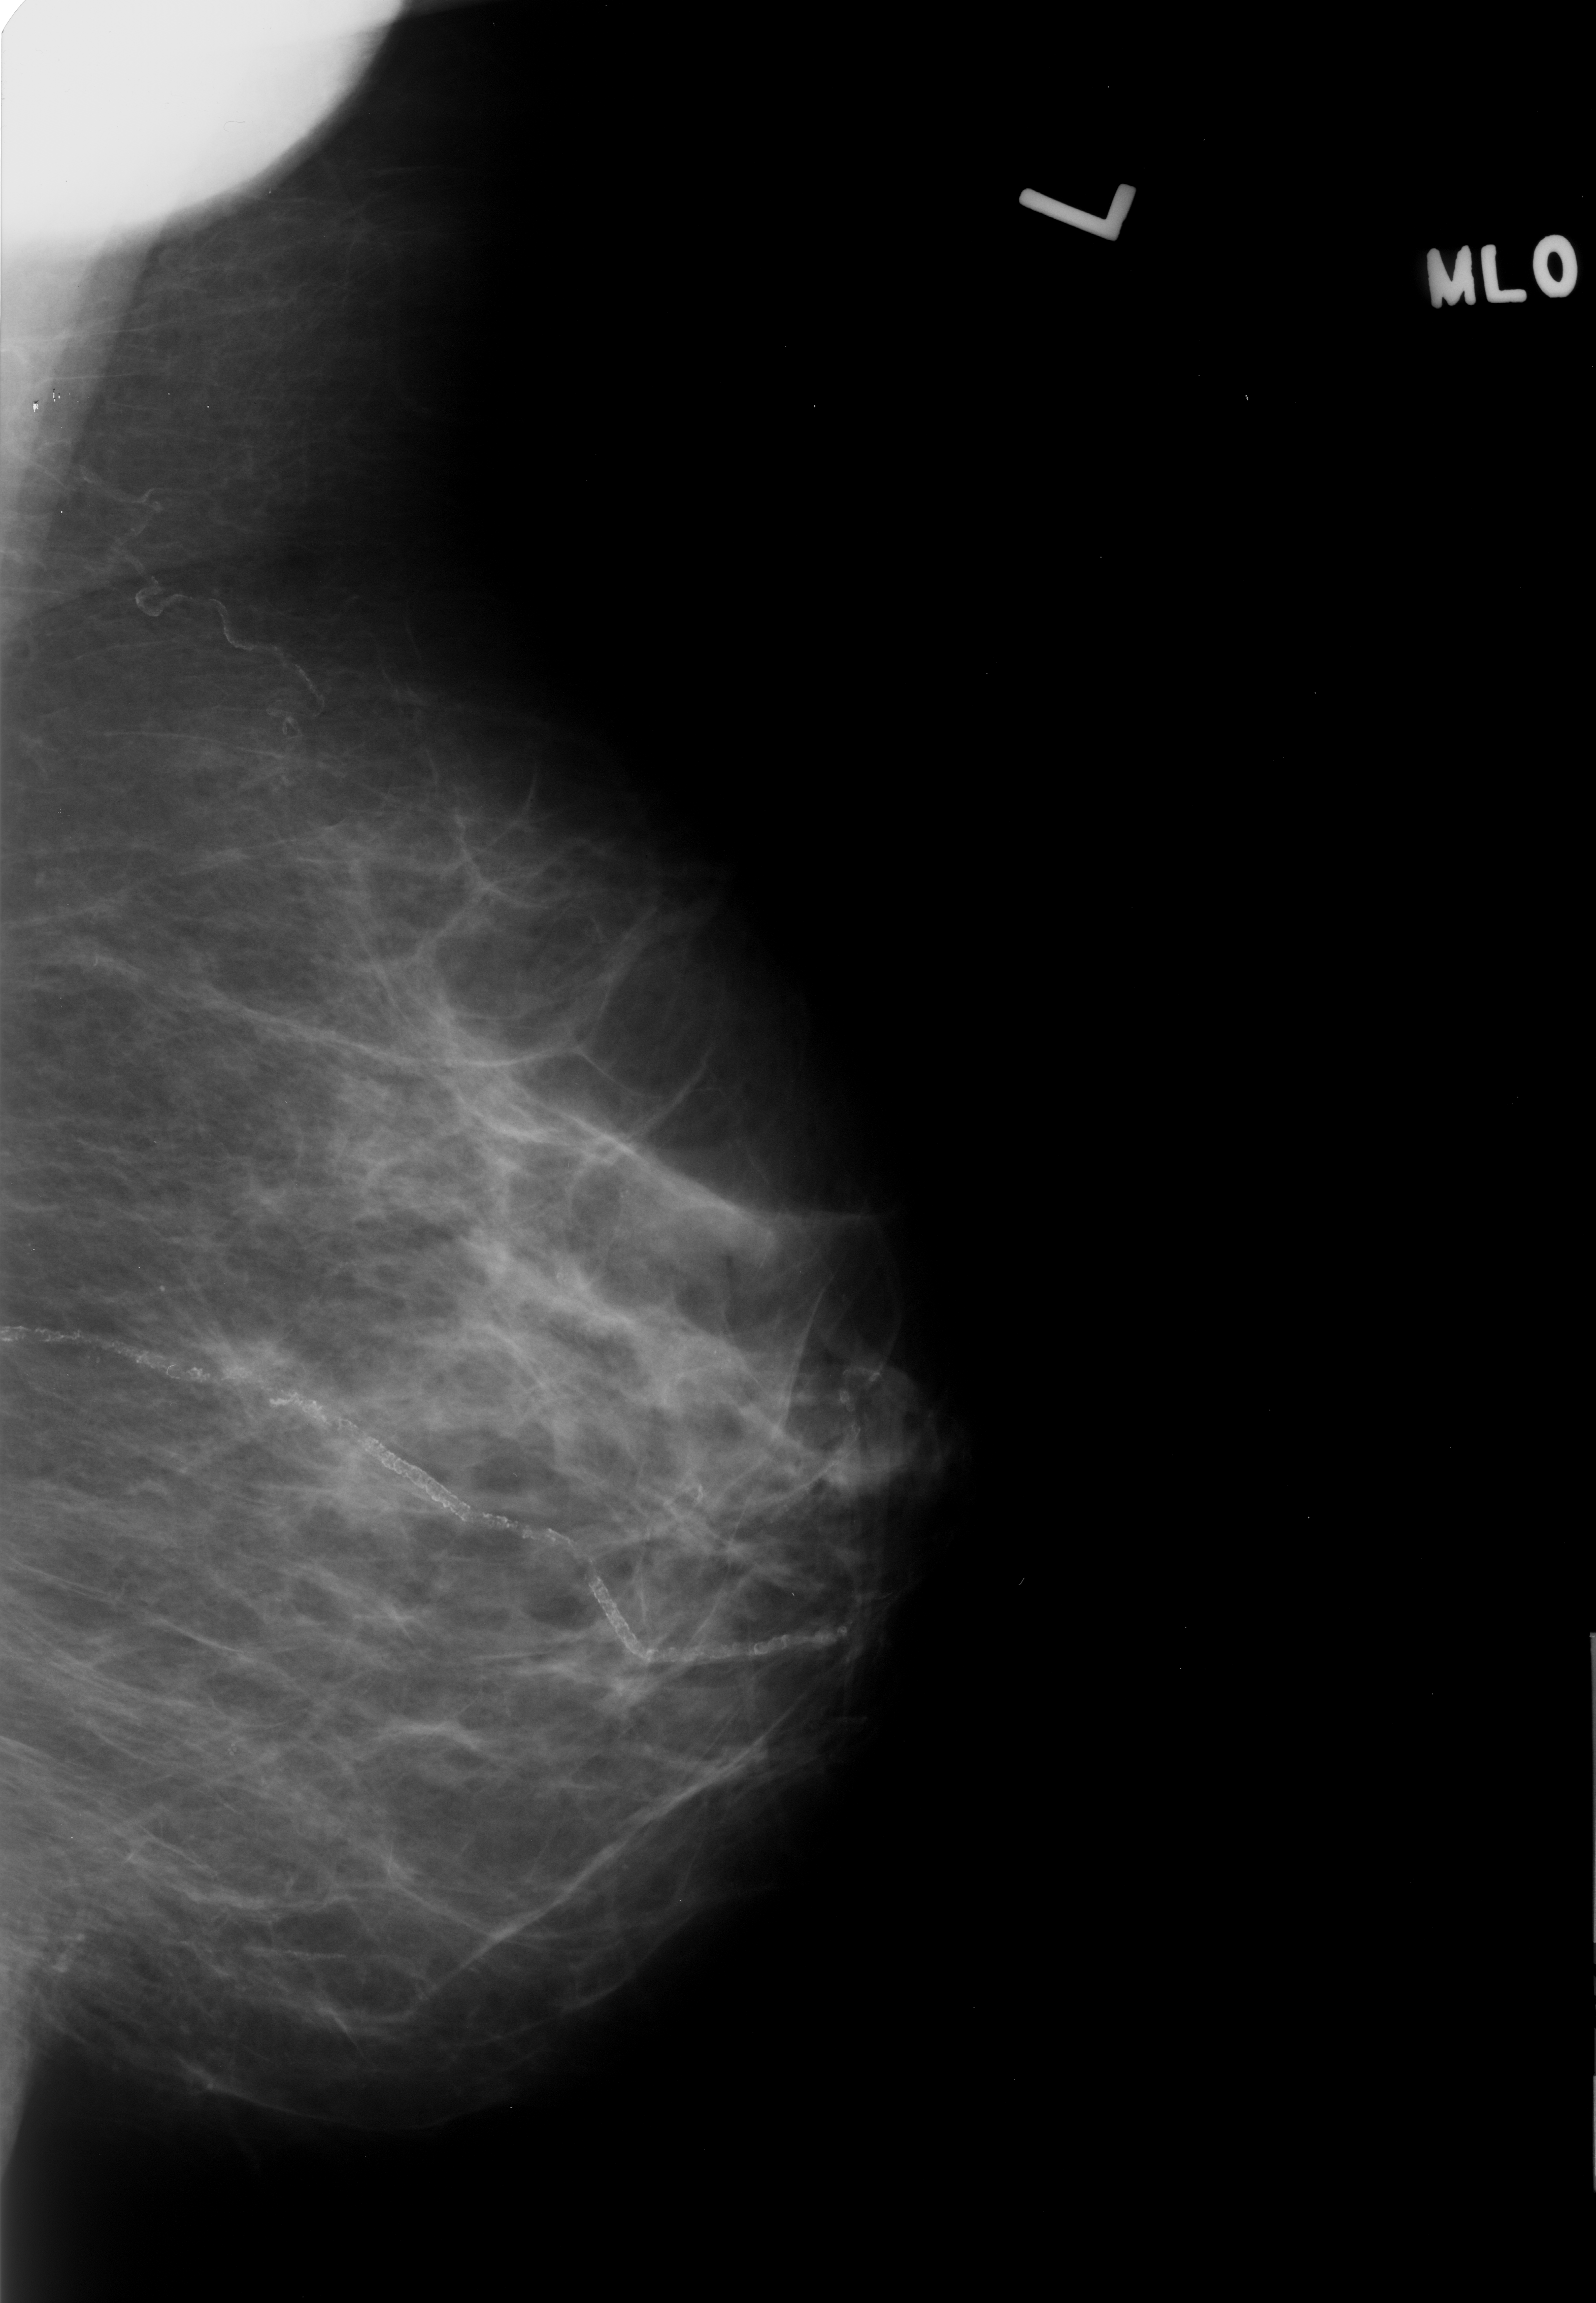
Digitized screen-film mammogram; left breast; mediolateral oblique (MLO) view; breast composition: scattered fibroglandular densities (BI-RADS density category 2 of 4).
Abnormality record for this image: Finding 1 of 2: calcifications, morphology pleomorphic, distribution clustered; BI-RADS assessment category 4; subtlety rating 2 on a 1 (subtle) to 5 (obvious) scale; pathology result (as recorded, not read from the image): benign. Finding 2 of 2: calcifications, morphology pleomorphic, distribution clustered; BI-RADS assessment category 4; pathology (as recorded): benign.